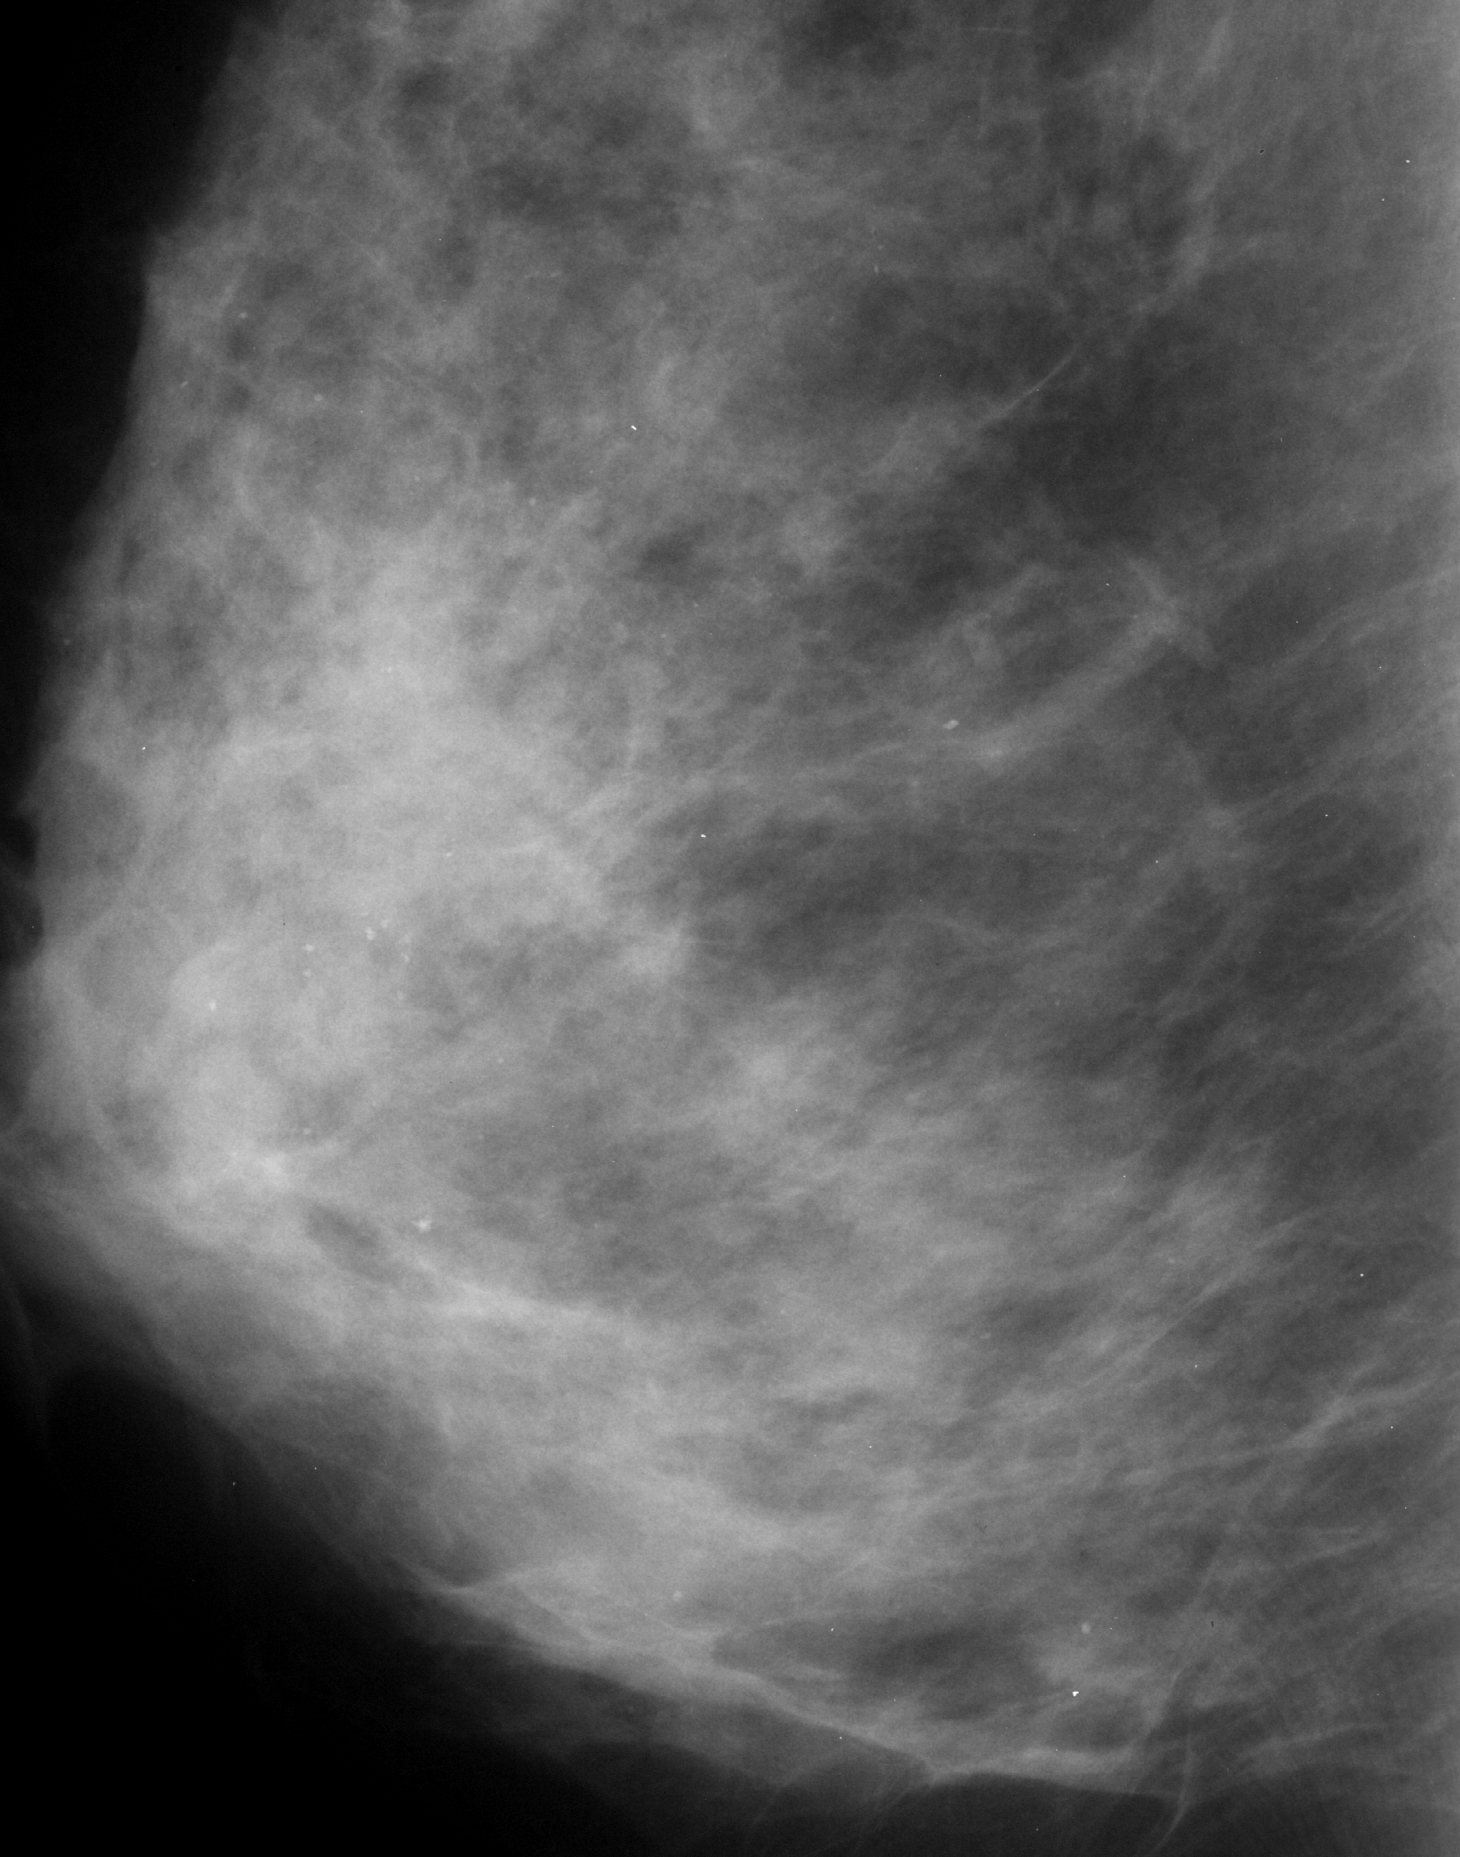
Region of interest cut from a scanned film mammogram (one marked finding), right breast, MLO view, BI-RADS breast density category 3 (scale 1–4).
Marked abnormality: calcifications, morphology pleomorphic, distribution diffusely scattered; BI-RADS assessment category 3; pathology result (as recorded, not read from the image): benign.